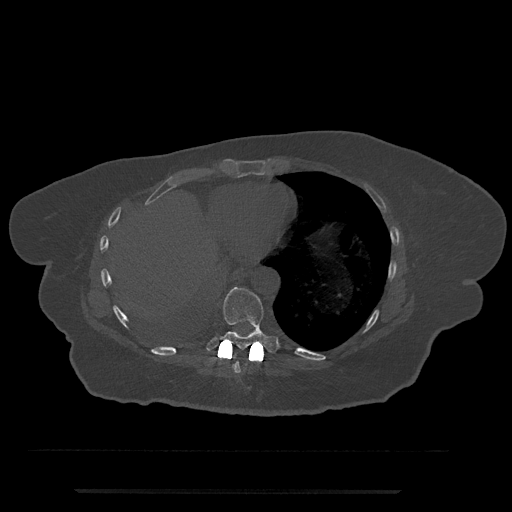
CT including the spine, one axial slice; position 341 of 797 along the scan axis; bone window (W 1800 / L 400 HU); 0.5 mm slice thickness; 512 × 512 image matrix, field of view 440 × 440 mm. Patient: female, 51 years. From the clinical record (not read from this slice): primary cancer: neuro; vertebrae with lytic lesions (as recorded): T8.
Structures marked on this image (semi-automatically segmented with operator editing):
- T8 vertebra: bounding box [x1, y1, x2, y2] px = [234, 353, 241, 373]
- T9 vertebra: [206, 287, 278, 353]